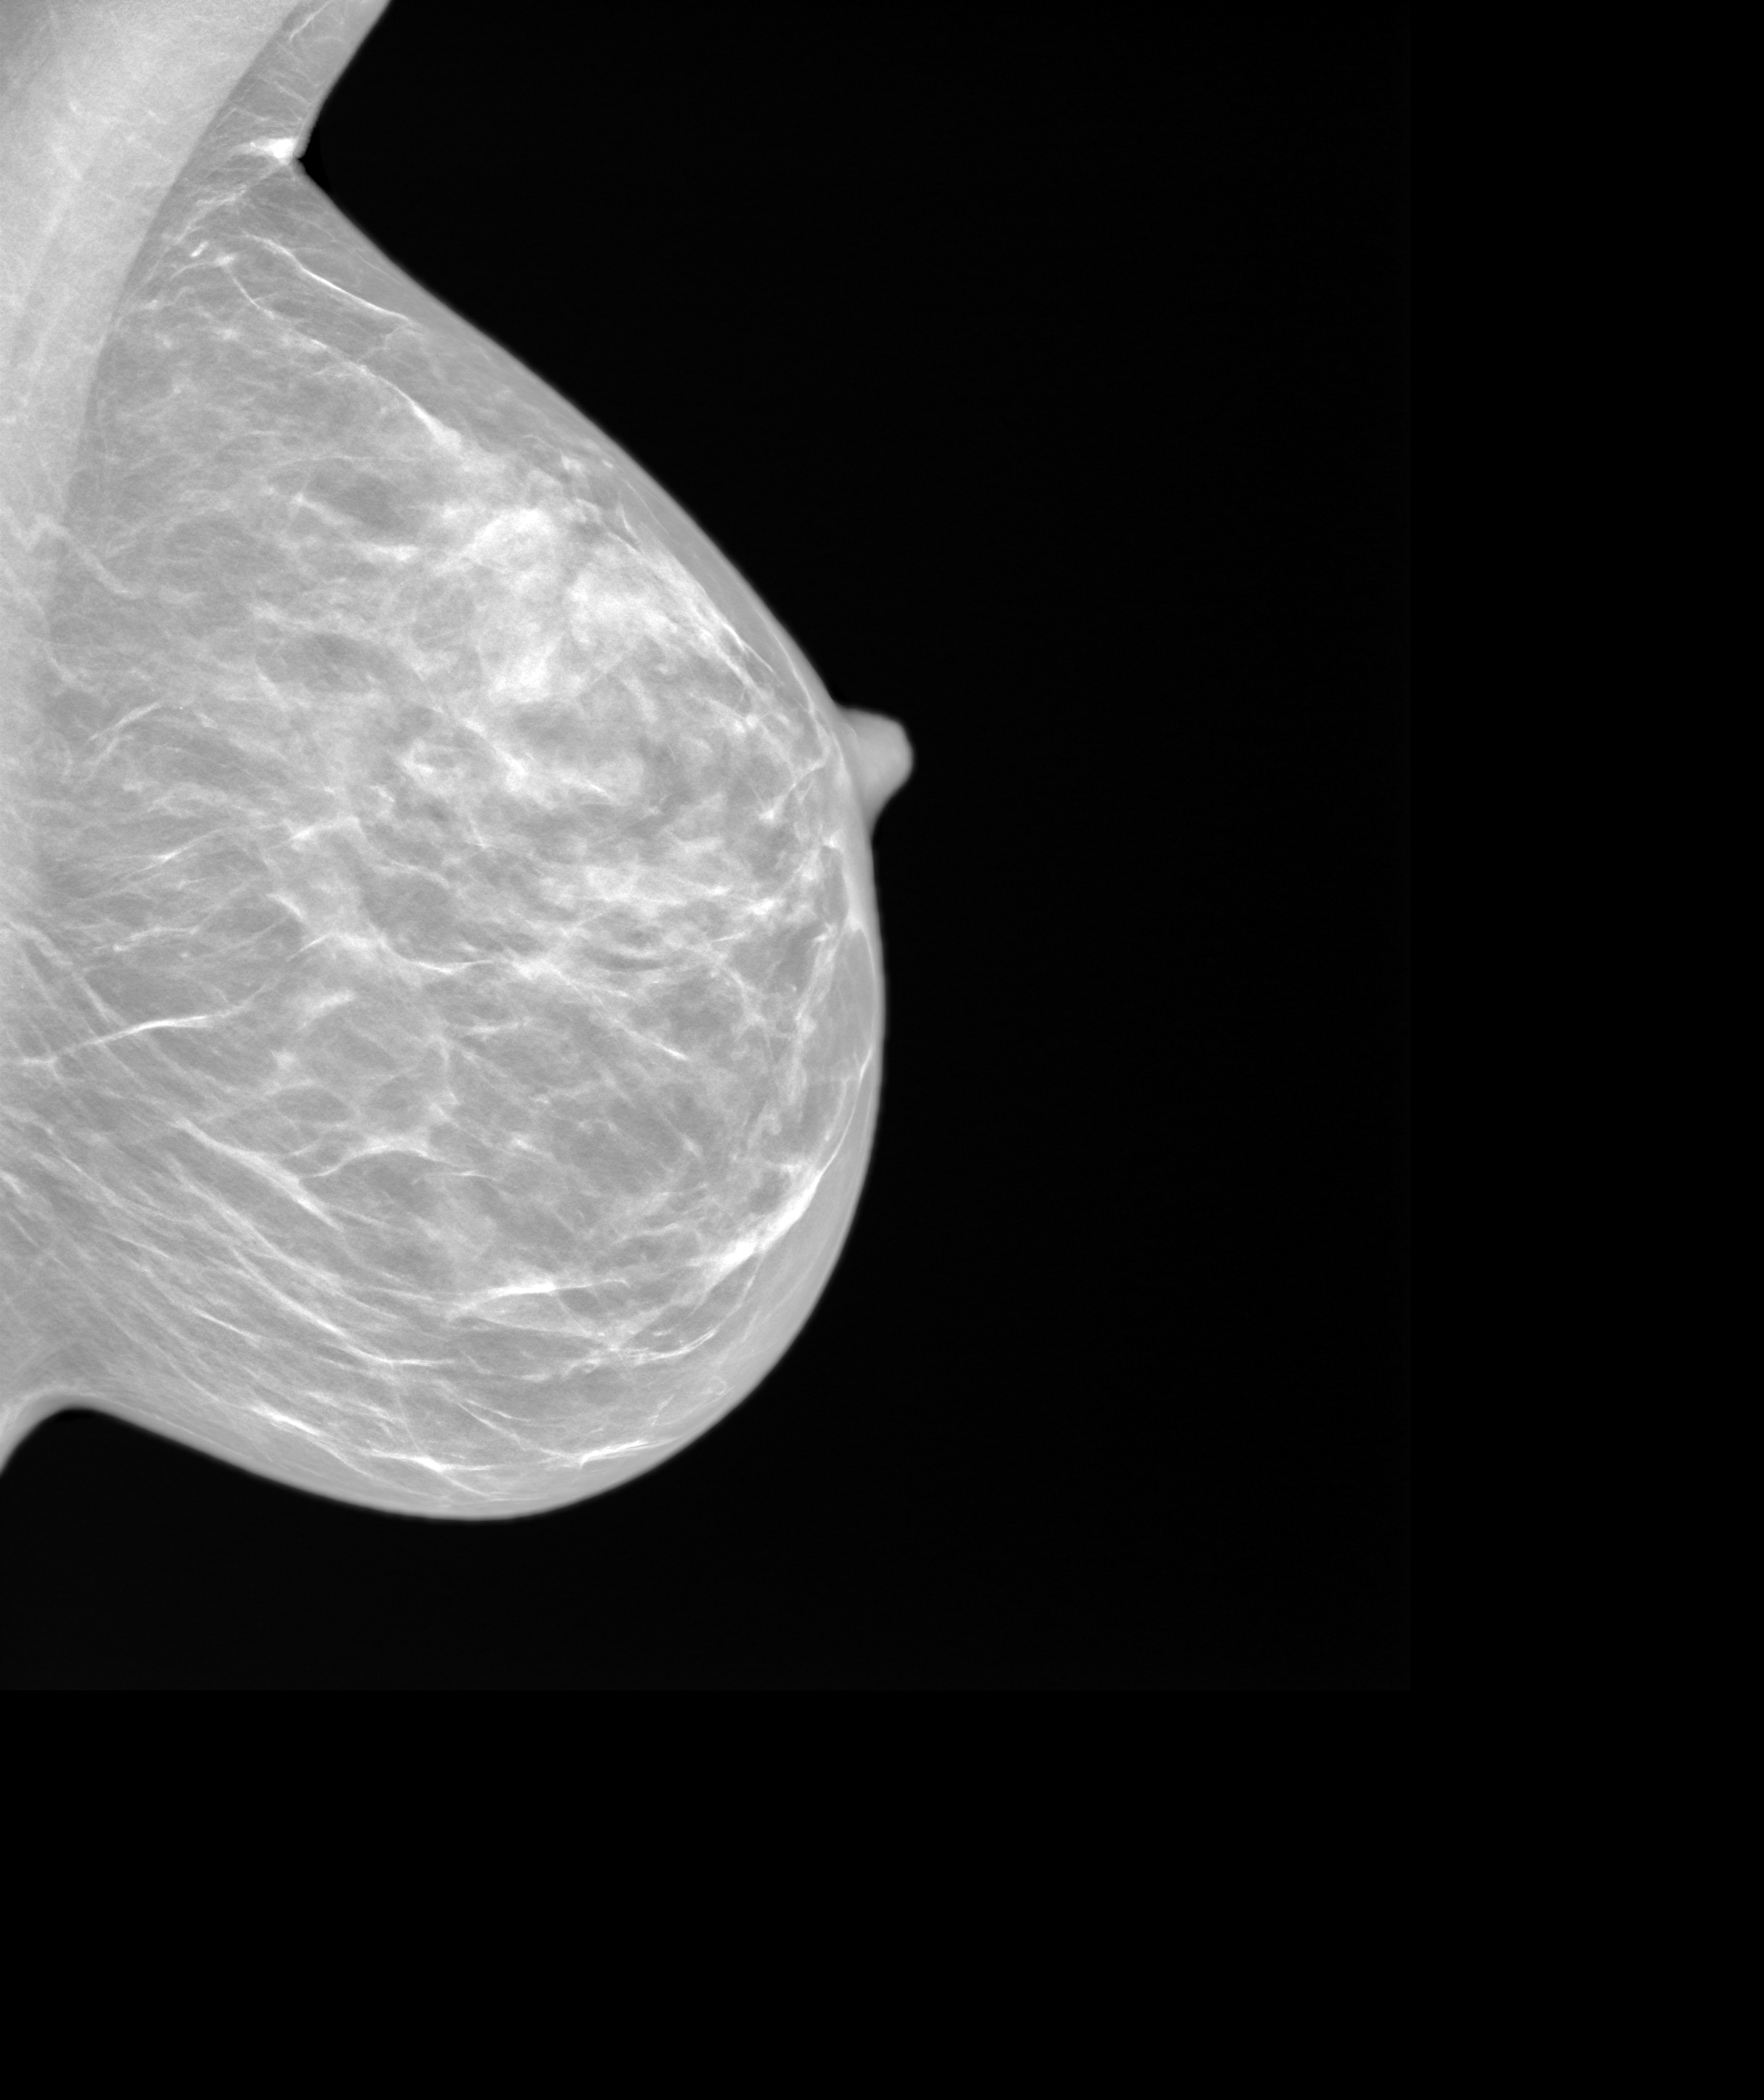
Screening examination, system: SenoIris_1SP1.1(421).
Image type: synthesized 2-D view from tomosynthesis. Breast: left. Projection: medio-lateral oblique projection.